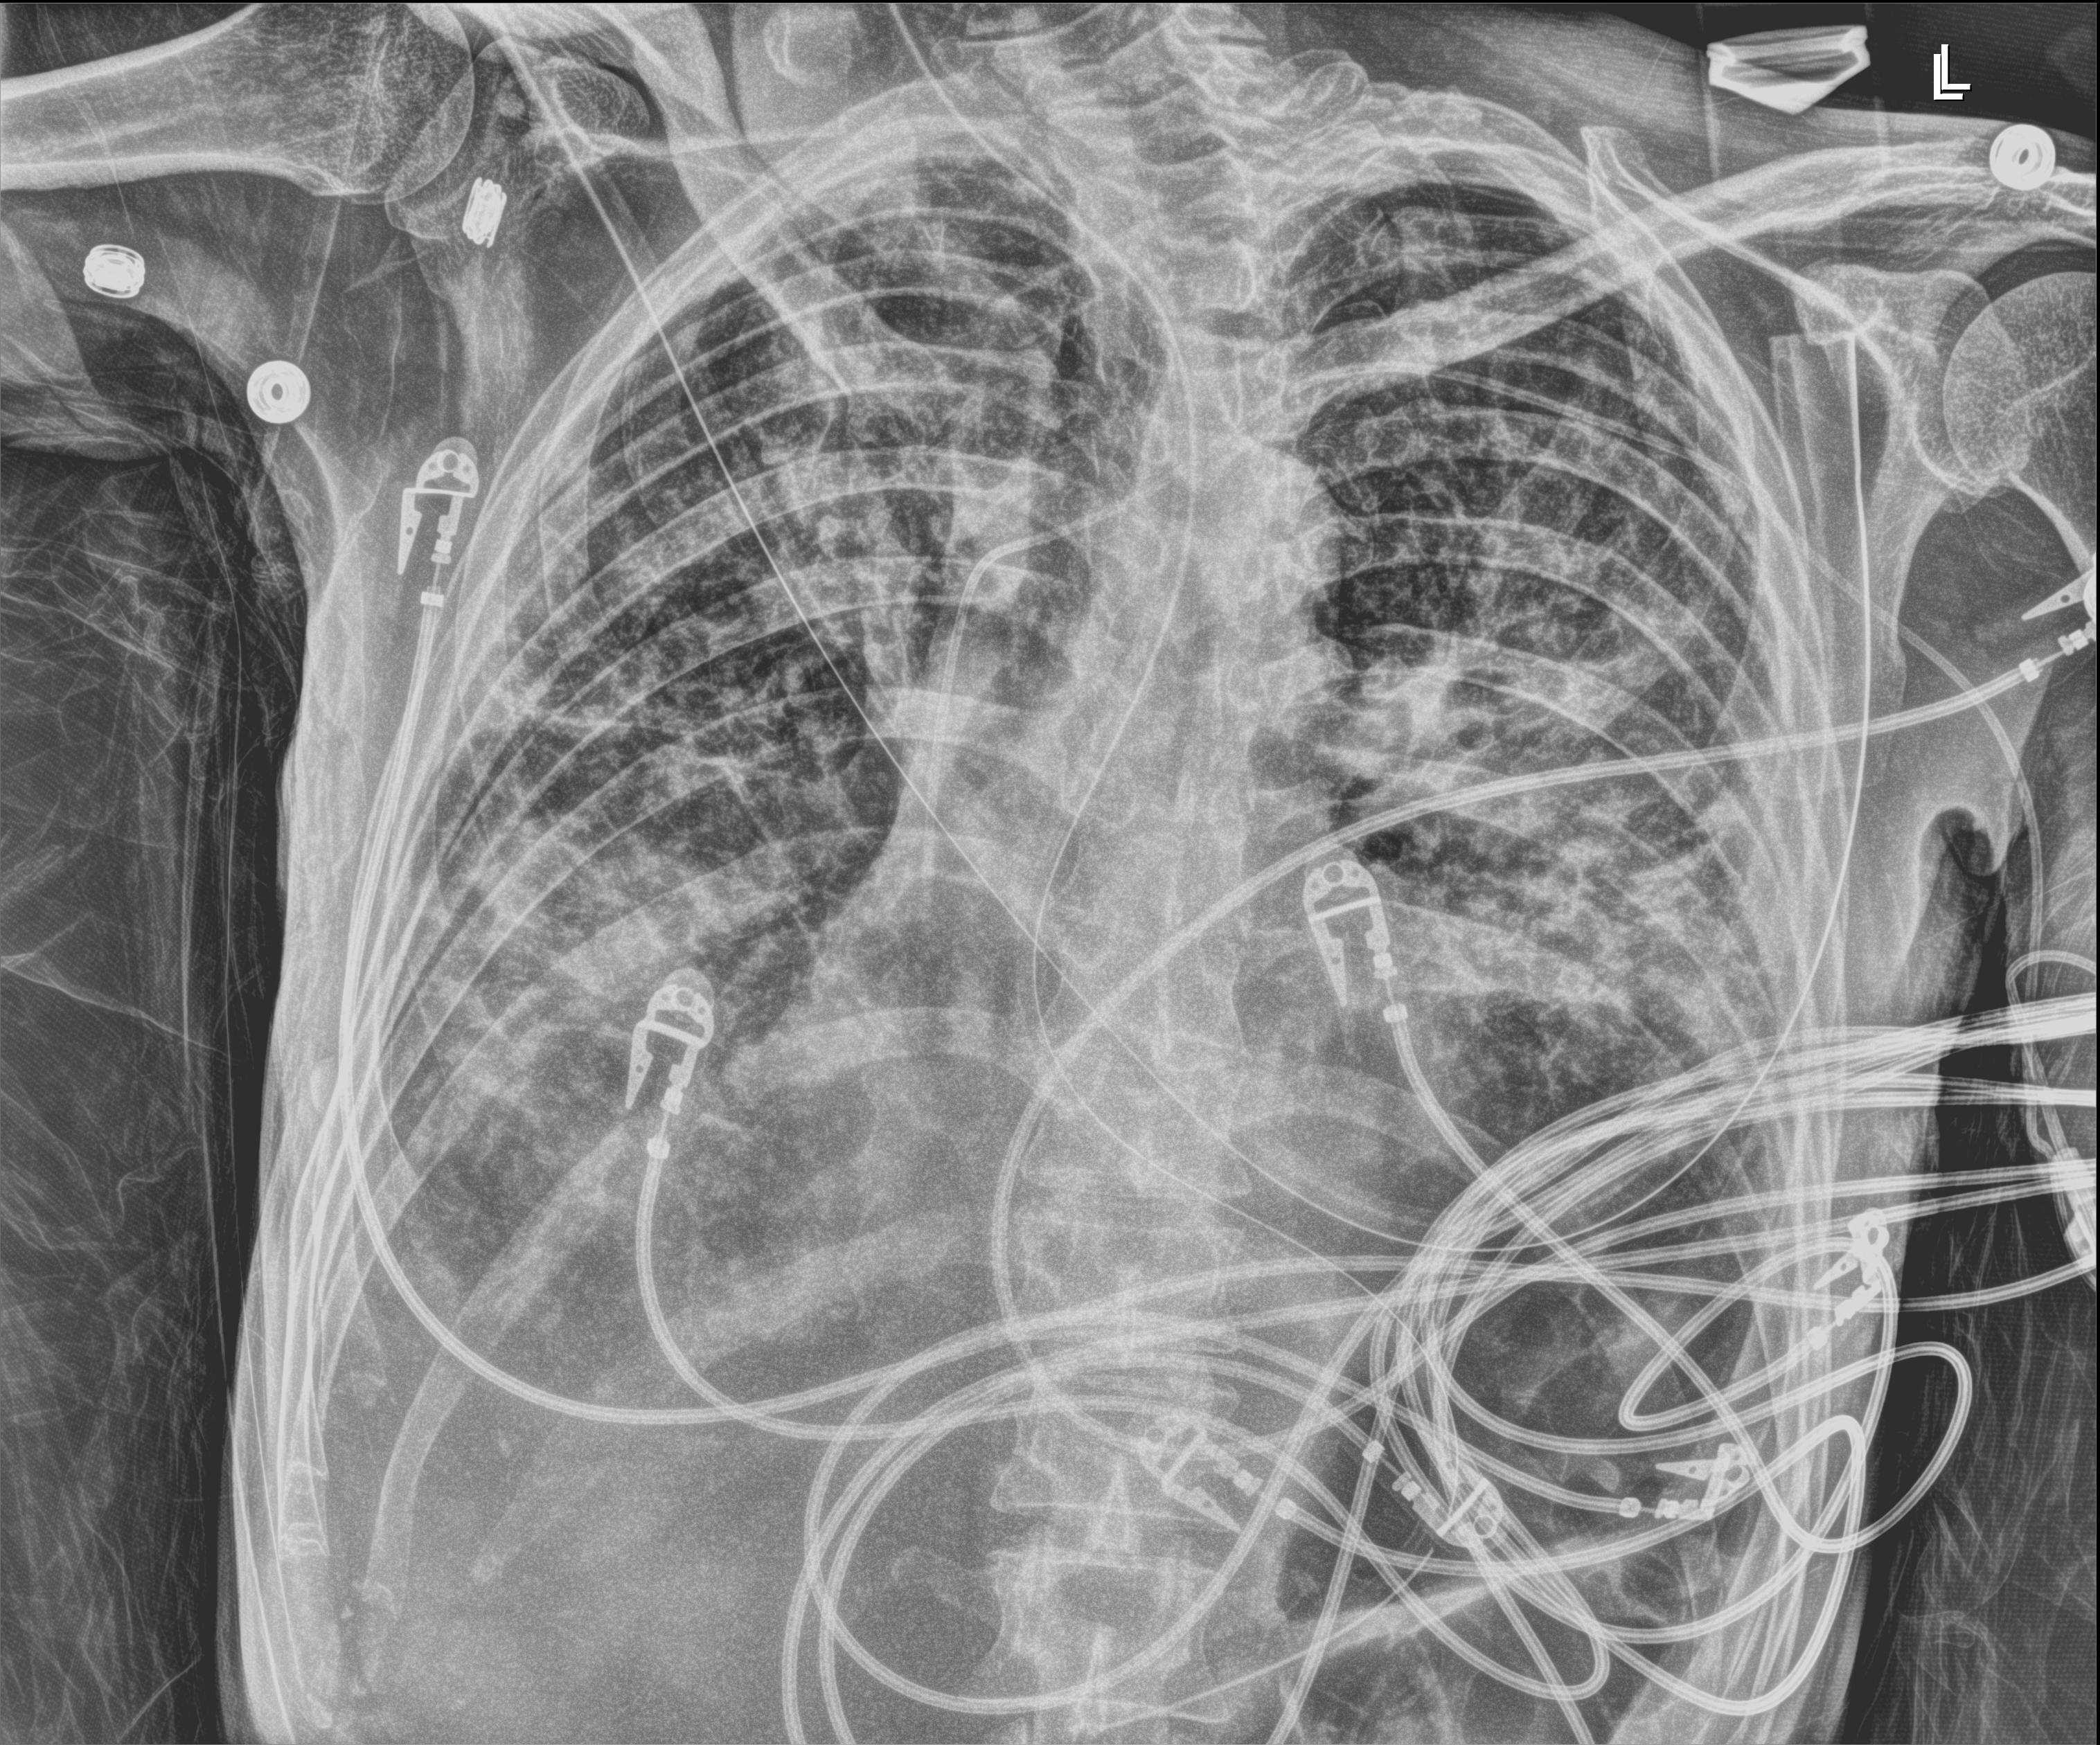
Chest radiograph (digital radiography), anteroposterior (AP) projection. Male patient hospitalised with COVID-19, age 18–59 years.
Hospital-stay facts (about this admission, not read from this image; timing relative to this image not recorded): mechanically ventilated during this hospital stay: yes; length of hospital stay: 96 days; admitted to intensive care during this hospital stay: yes.